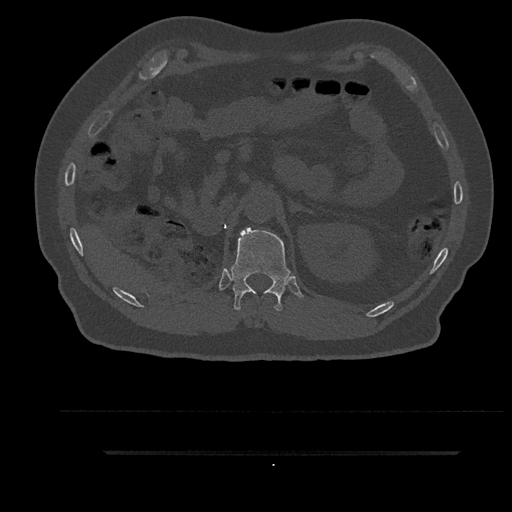
CT including the spine, one axial slice; position 249 of 797 along the scan axis; bone window (W 1800 / L 400 HU); 512 × 512 image matrix, field of view 432 × 432 mm. Male patient, age 63 years. Case-level facts recorded for this patient, not image findings: primary cancer: renal.
Structures marked on this image (semi-automatic segmentation, software-assisted and operator-edited):
- T12 vertebra: bounding box (x1, y1, x2, y2) in pixels: (229, 227, 292, 311)